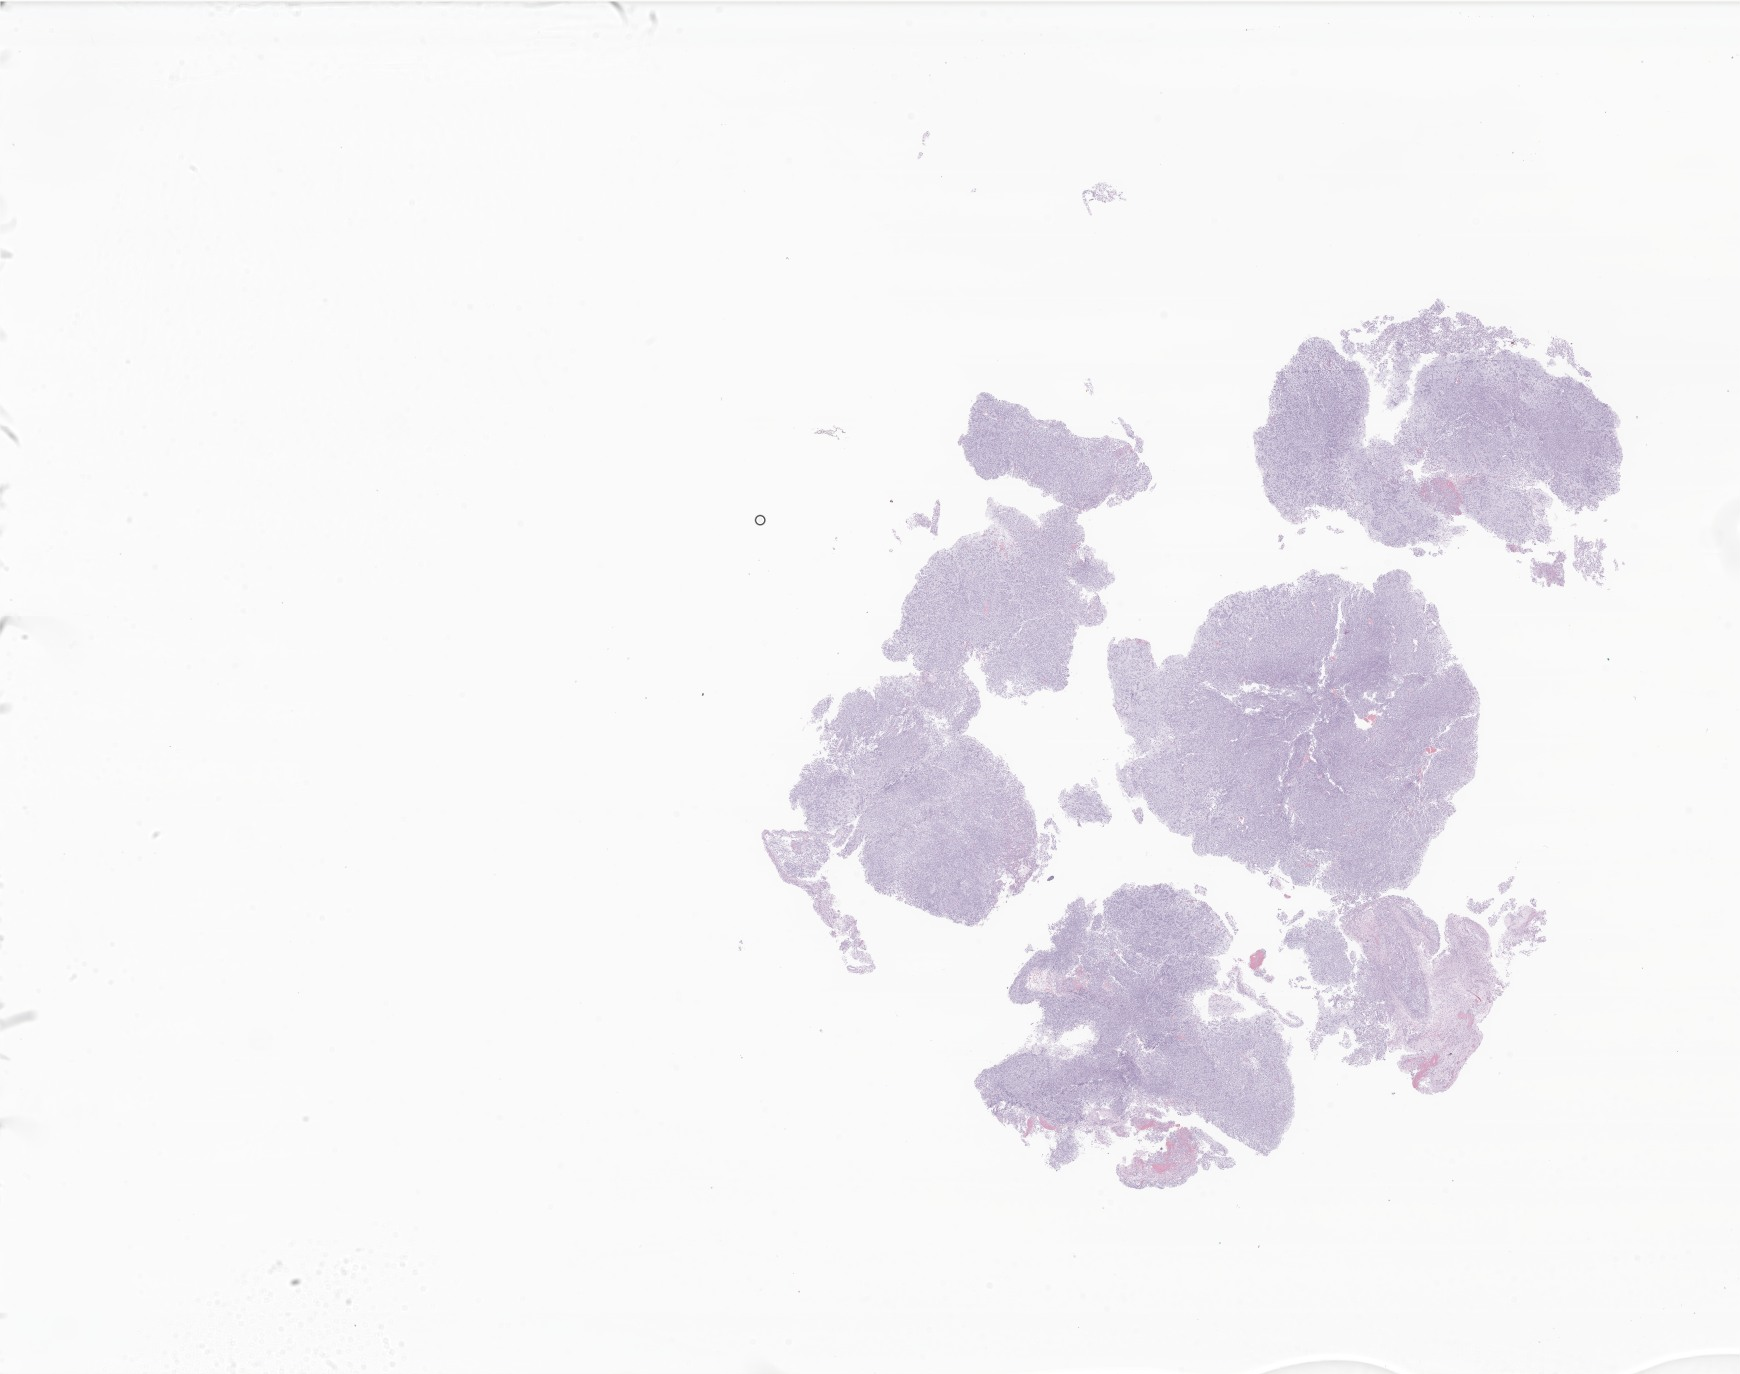
Whole-slide image, H&E stain of tumor tissue from the brain, shown as a low-resolution overview of the whole scanned area (about 29.3 x 23.2 mm); FFPE section. Patient: male, age 162 months.
• diagnosis (ICD-O-3 morphology term): Neoplasm, uncertain whether benign or malignant